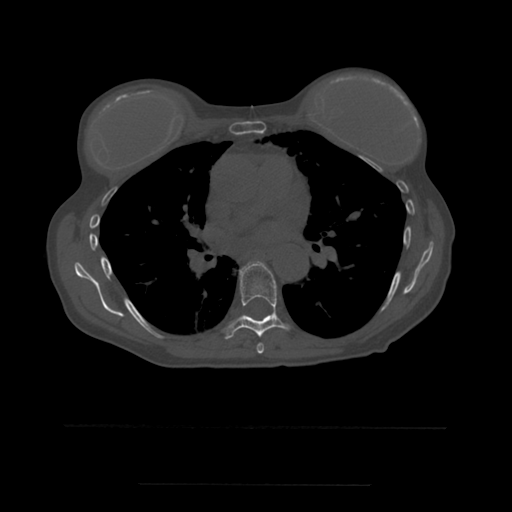
CT including the spine, one axial slice; position 359 of 544 along the scan axis; bone window (W 1800 / L 400 HU); 512 × 512 image matrix, field of view 350 × 350 mm. Patient age 58 years. Case-level facts recorded for this patient, not image findings: primary cancer: lung.
Structures marked on this image (semi-automatically segmented with operator editing):
- T6 vertebra: bounding box <257,343,264,354> (left, top, right, bottom; pixels)
- T7 vertebra: <226,263,290,340>